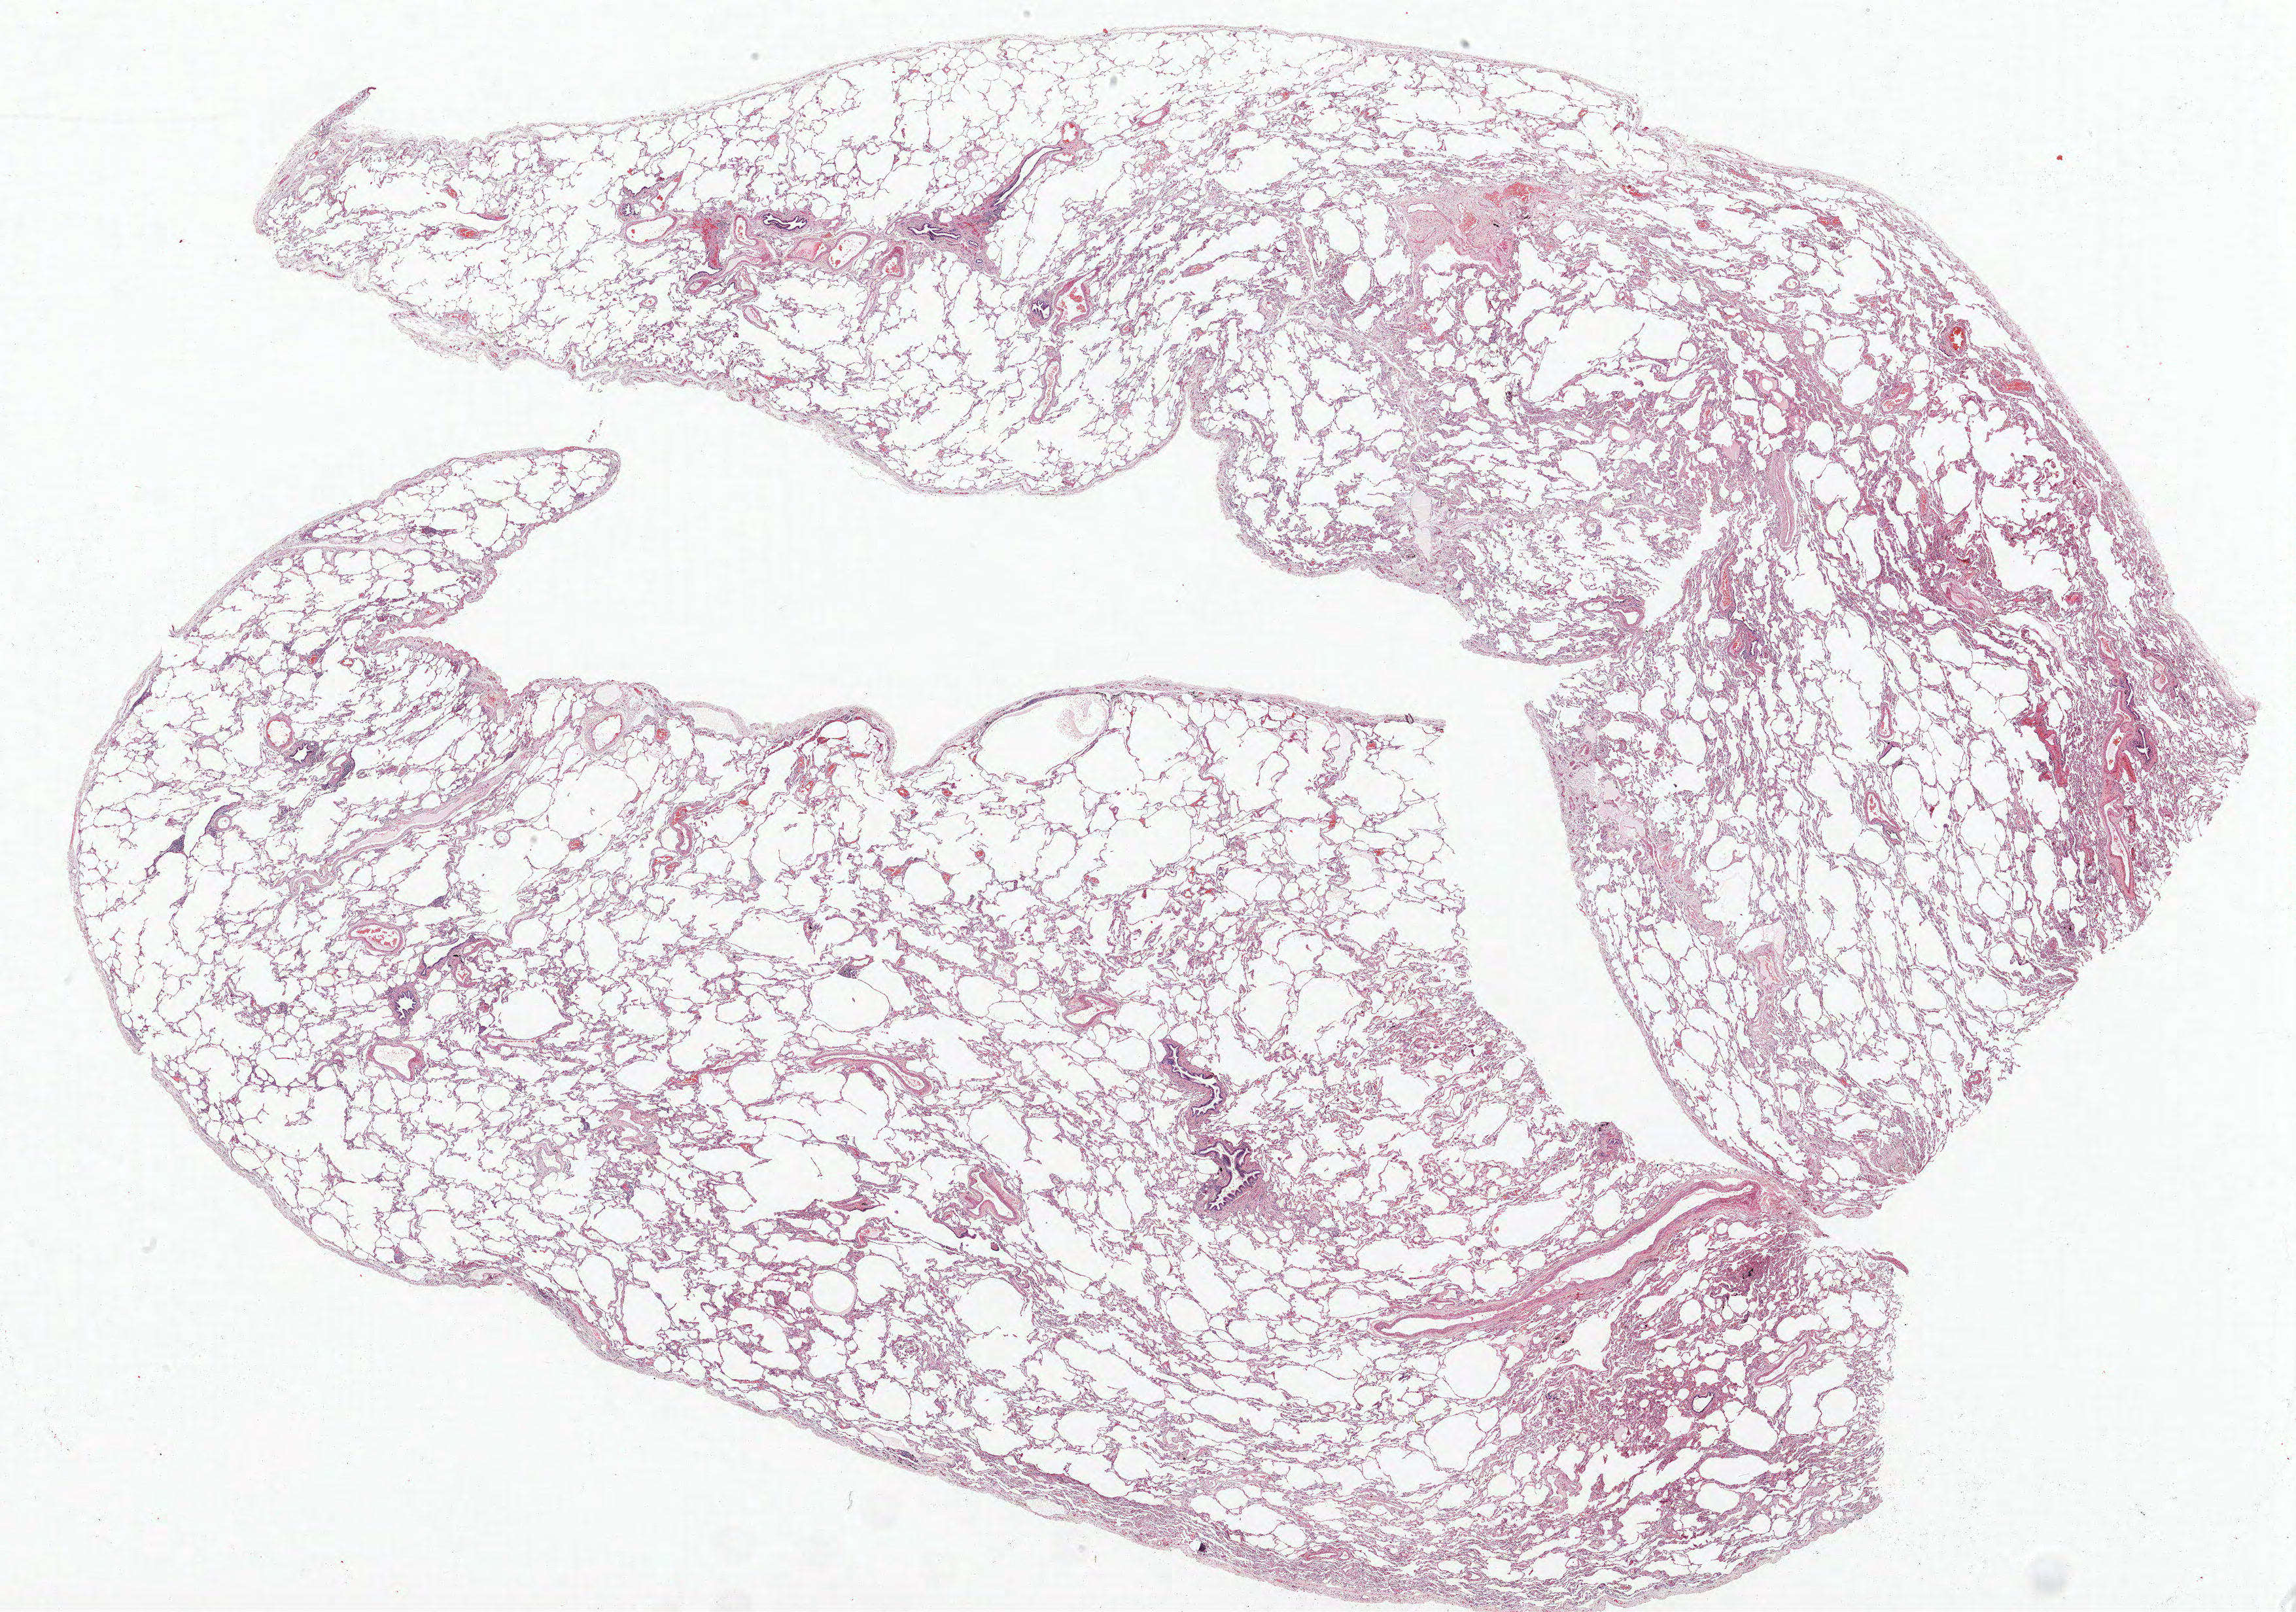
Whole-slide histology image, H&E, low-resolution overview of the scanned area, about 28.1 x 19.7 mm, FFPE section, lung. Female patient, aged 68 at enrolment. Former smoker at enrolment. Grade: well differentiated (G1).
Stage (AJCC 6th edition): IA. Primary tumour location (clinical record): right lower lobe. Tumour size (pathology): 15 mm. Participant's lung-cancer diagnosis: Bronchiolo-alveolar adenocarcinoma, NOS.